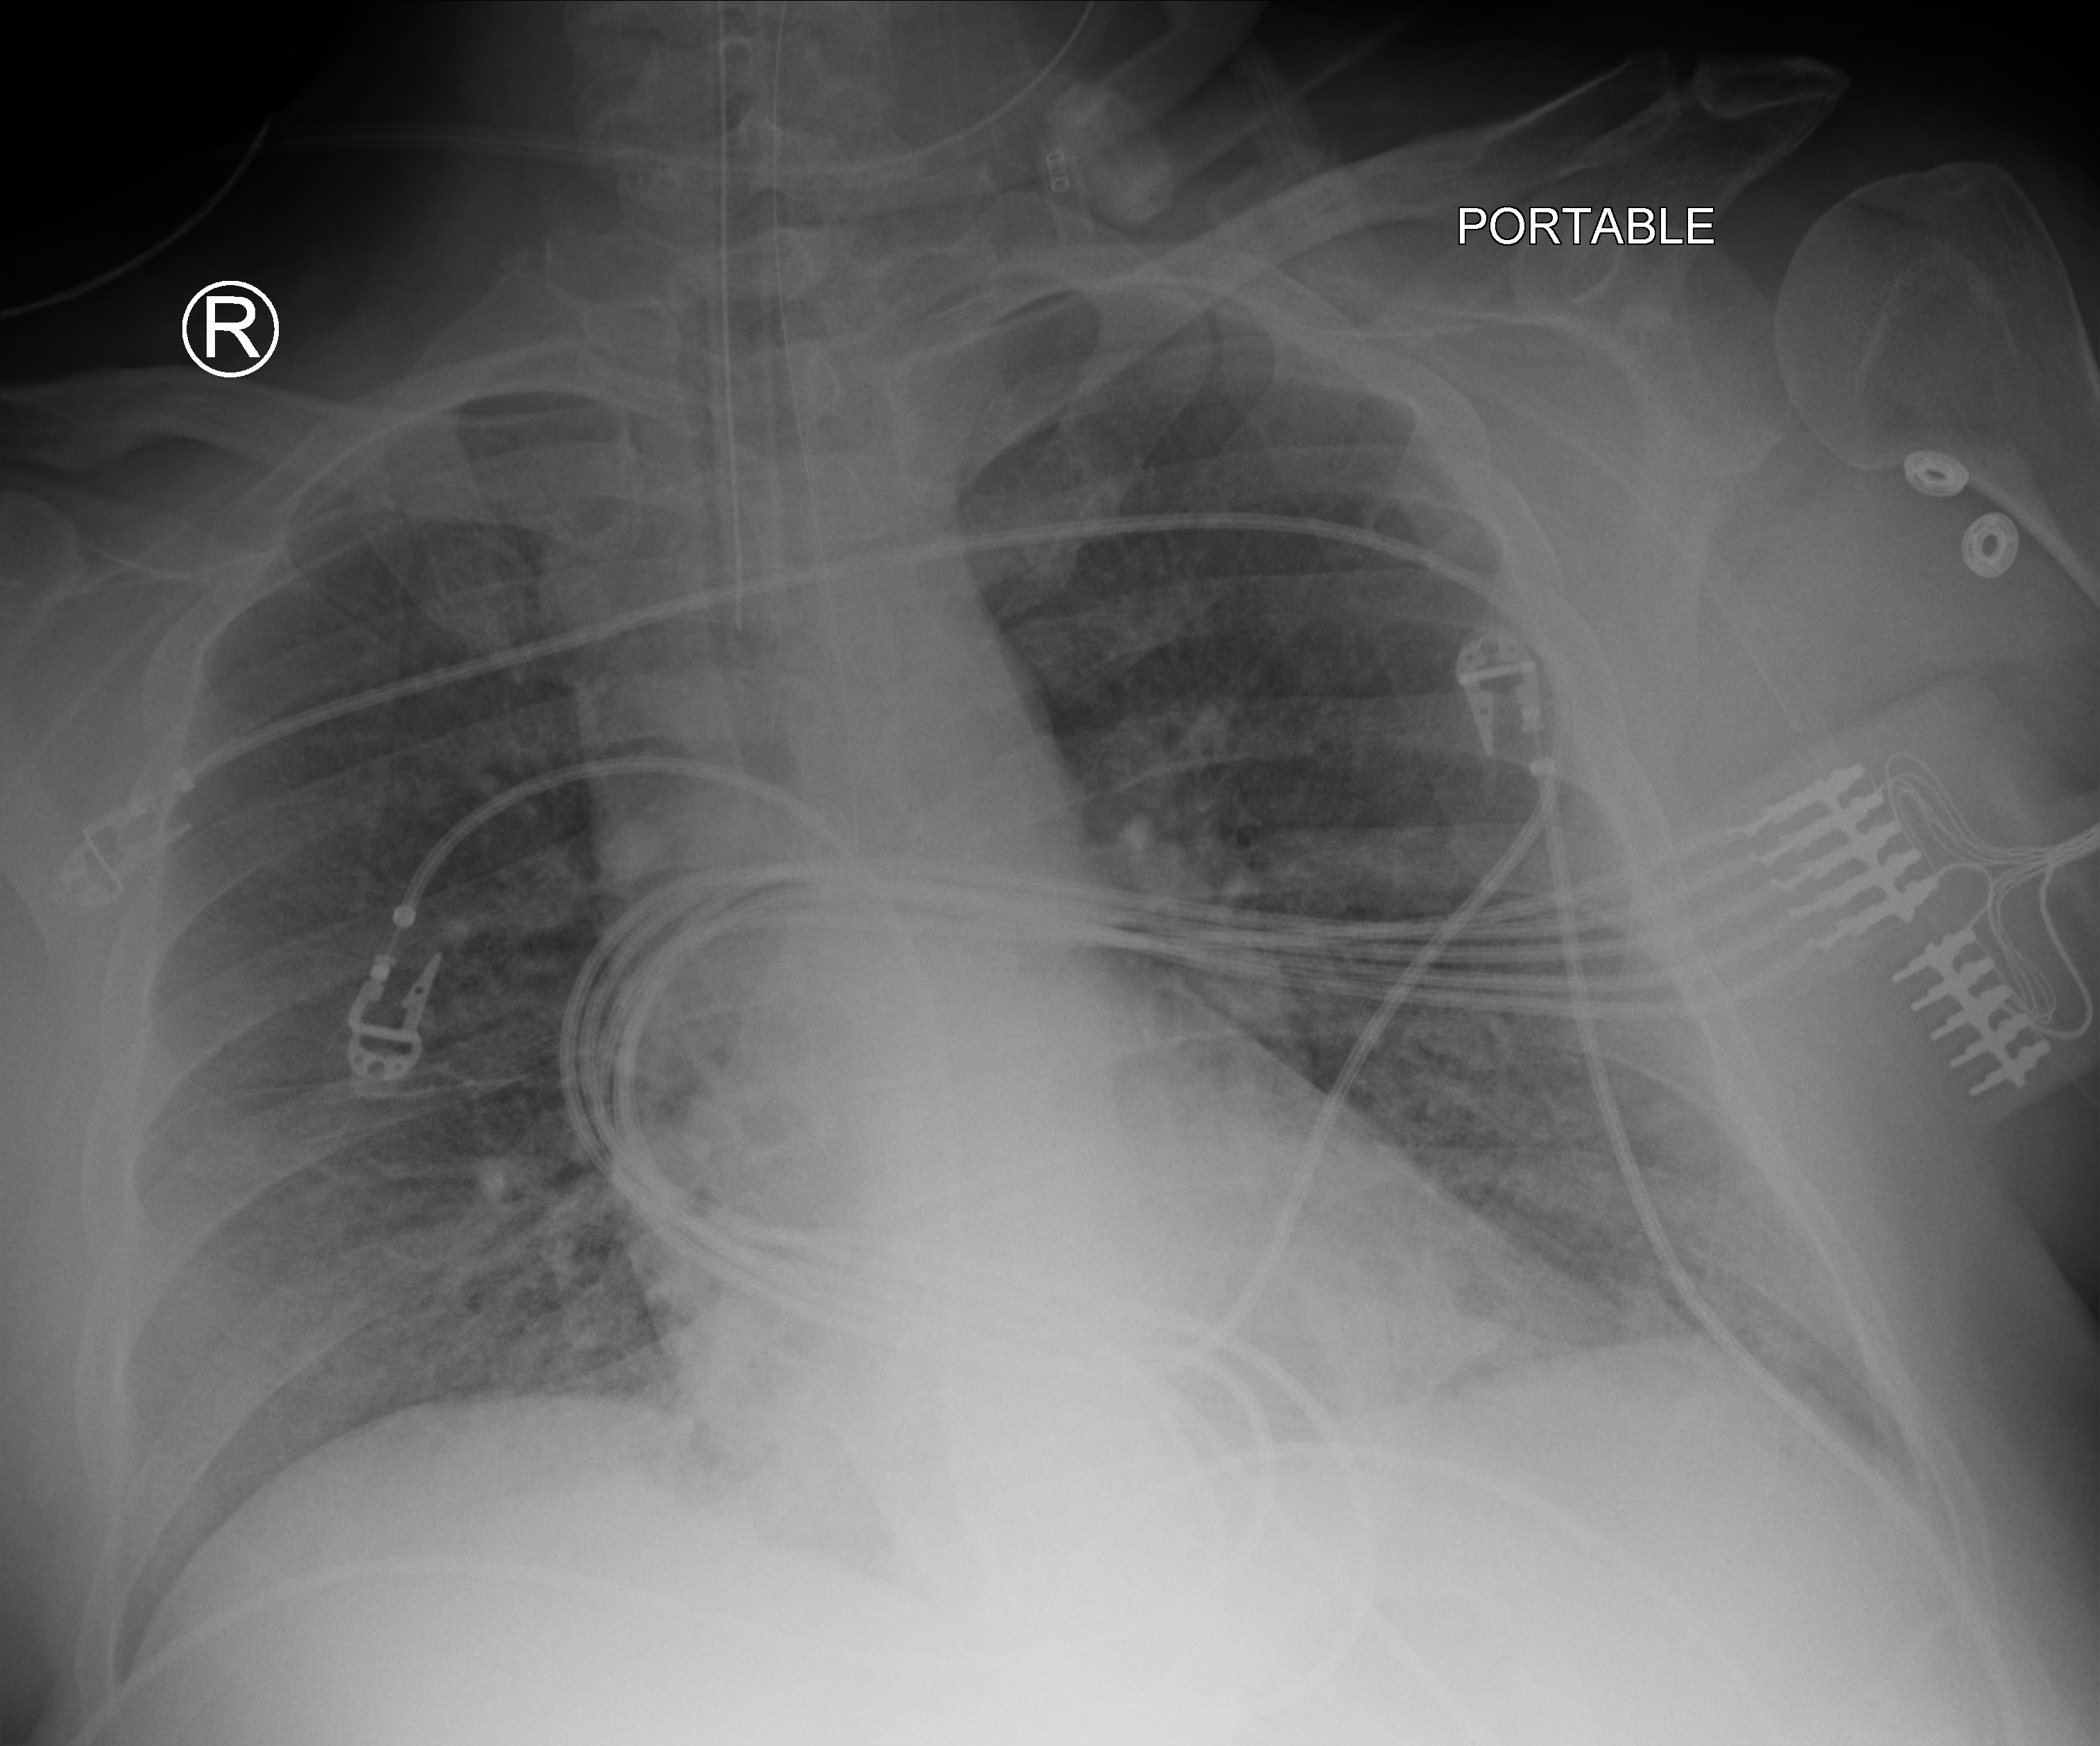
Portable chest radiograph, anteroposterior (AP) projection. Patient hospitalised with COVID-19, aged 18–59 years.
Admission-level facts for this patient (not findings on this image; timing relative to this image not recorded): length of hospital stay: 26 days; mechanically ventilated during this hospital stay: yes; admitted to intensive care during this hospital stay: yes.